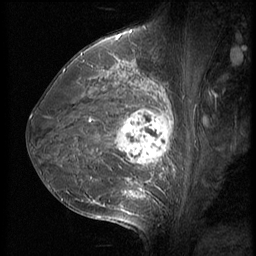
Breast MRI (dynamic contrast-enhanced), one sagittal slice; slice 35 of 56 in the series (ordered by position); 3 images stored at this slice position (order not interpretable as contrast timing); 1.5 T; TE 4.2 ms, TR 9 ms; 2.5 mm slice thickness; 256 × 256 image matrix, field of view 180 × 180 mm. Patient: female, 35 years. From the clinical record (not read from this slice): setting: breast cancer imaged before/during neoadjuvant chemotherapy; receptor status: HR-positive, HER2-negative.
Outlined on this slice (semi-automatic segmentation, software-assisted and operator-edited):
- analysis volume of interest (the breast-tissue region the enhancement analysis was run in; not a lesion): bounding box [x1, y1, x2, y2] px = [63, 60, 190, 218]
- tumour enhancement mask (voxels above the 140 % enhancement threshold inside the analysis volume of interest): [109, 84, 173, 199]